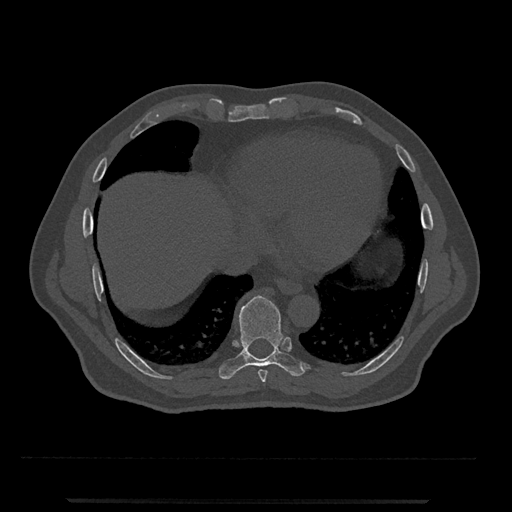
CT including the spine, one axial slice. Position 584 of 797 along the scan axis. 120 kVp. Bone window (W 1800 / L 400 HU). 0.5 mm slice thickness. 512 × 512 image matrix, field of view 419 × 419 mm. Male patient, age 63 years. From the clinical record (not read from this slice): primary cancer: prostate.
Structures marked on this image (semi-automatically segmented with operator editing):
- T8 vertebra: bounding box <258,370,268,383> (left, top, right, bottom; pixels)
- T9 vertebra: <219,295,306,380>